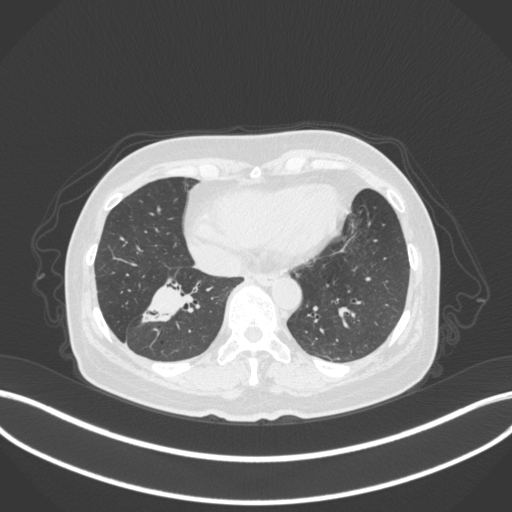
Chest CT, one axial slice. Position 122 of 429 along the scan axis. Reconstruction kernel B31f. Lung window (W 1500 / L -600 HU). 1 mm slice thickness. 512 × 512 image matrix, field of view 400 × 400 mm. Female patient, age 67 years. From the clinical record (not read from this slice): clinical TNM (as recorded): T1c N1 M0.
Outlined on this slice (bounding box drawn by a radiologist):
- lung tumour (recorded histology: adenocarcinoma): bounding box (x1, y1, x2, y2) in pixels: (140, 274, 207, 331)